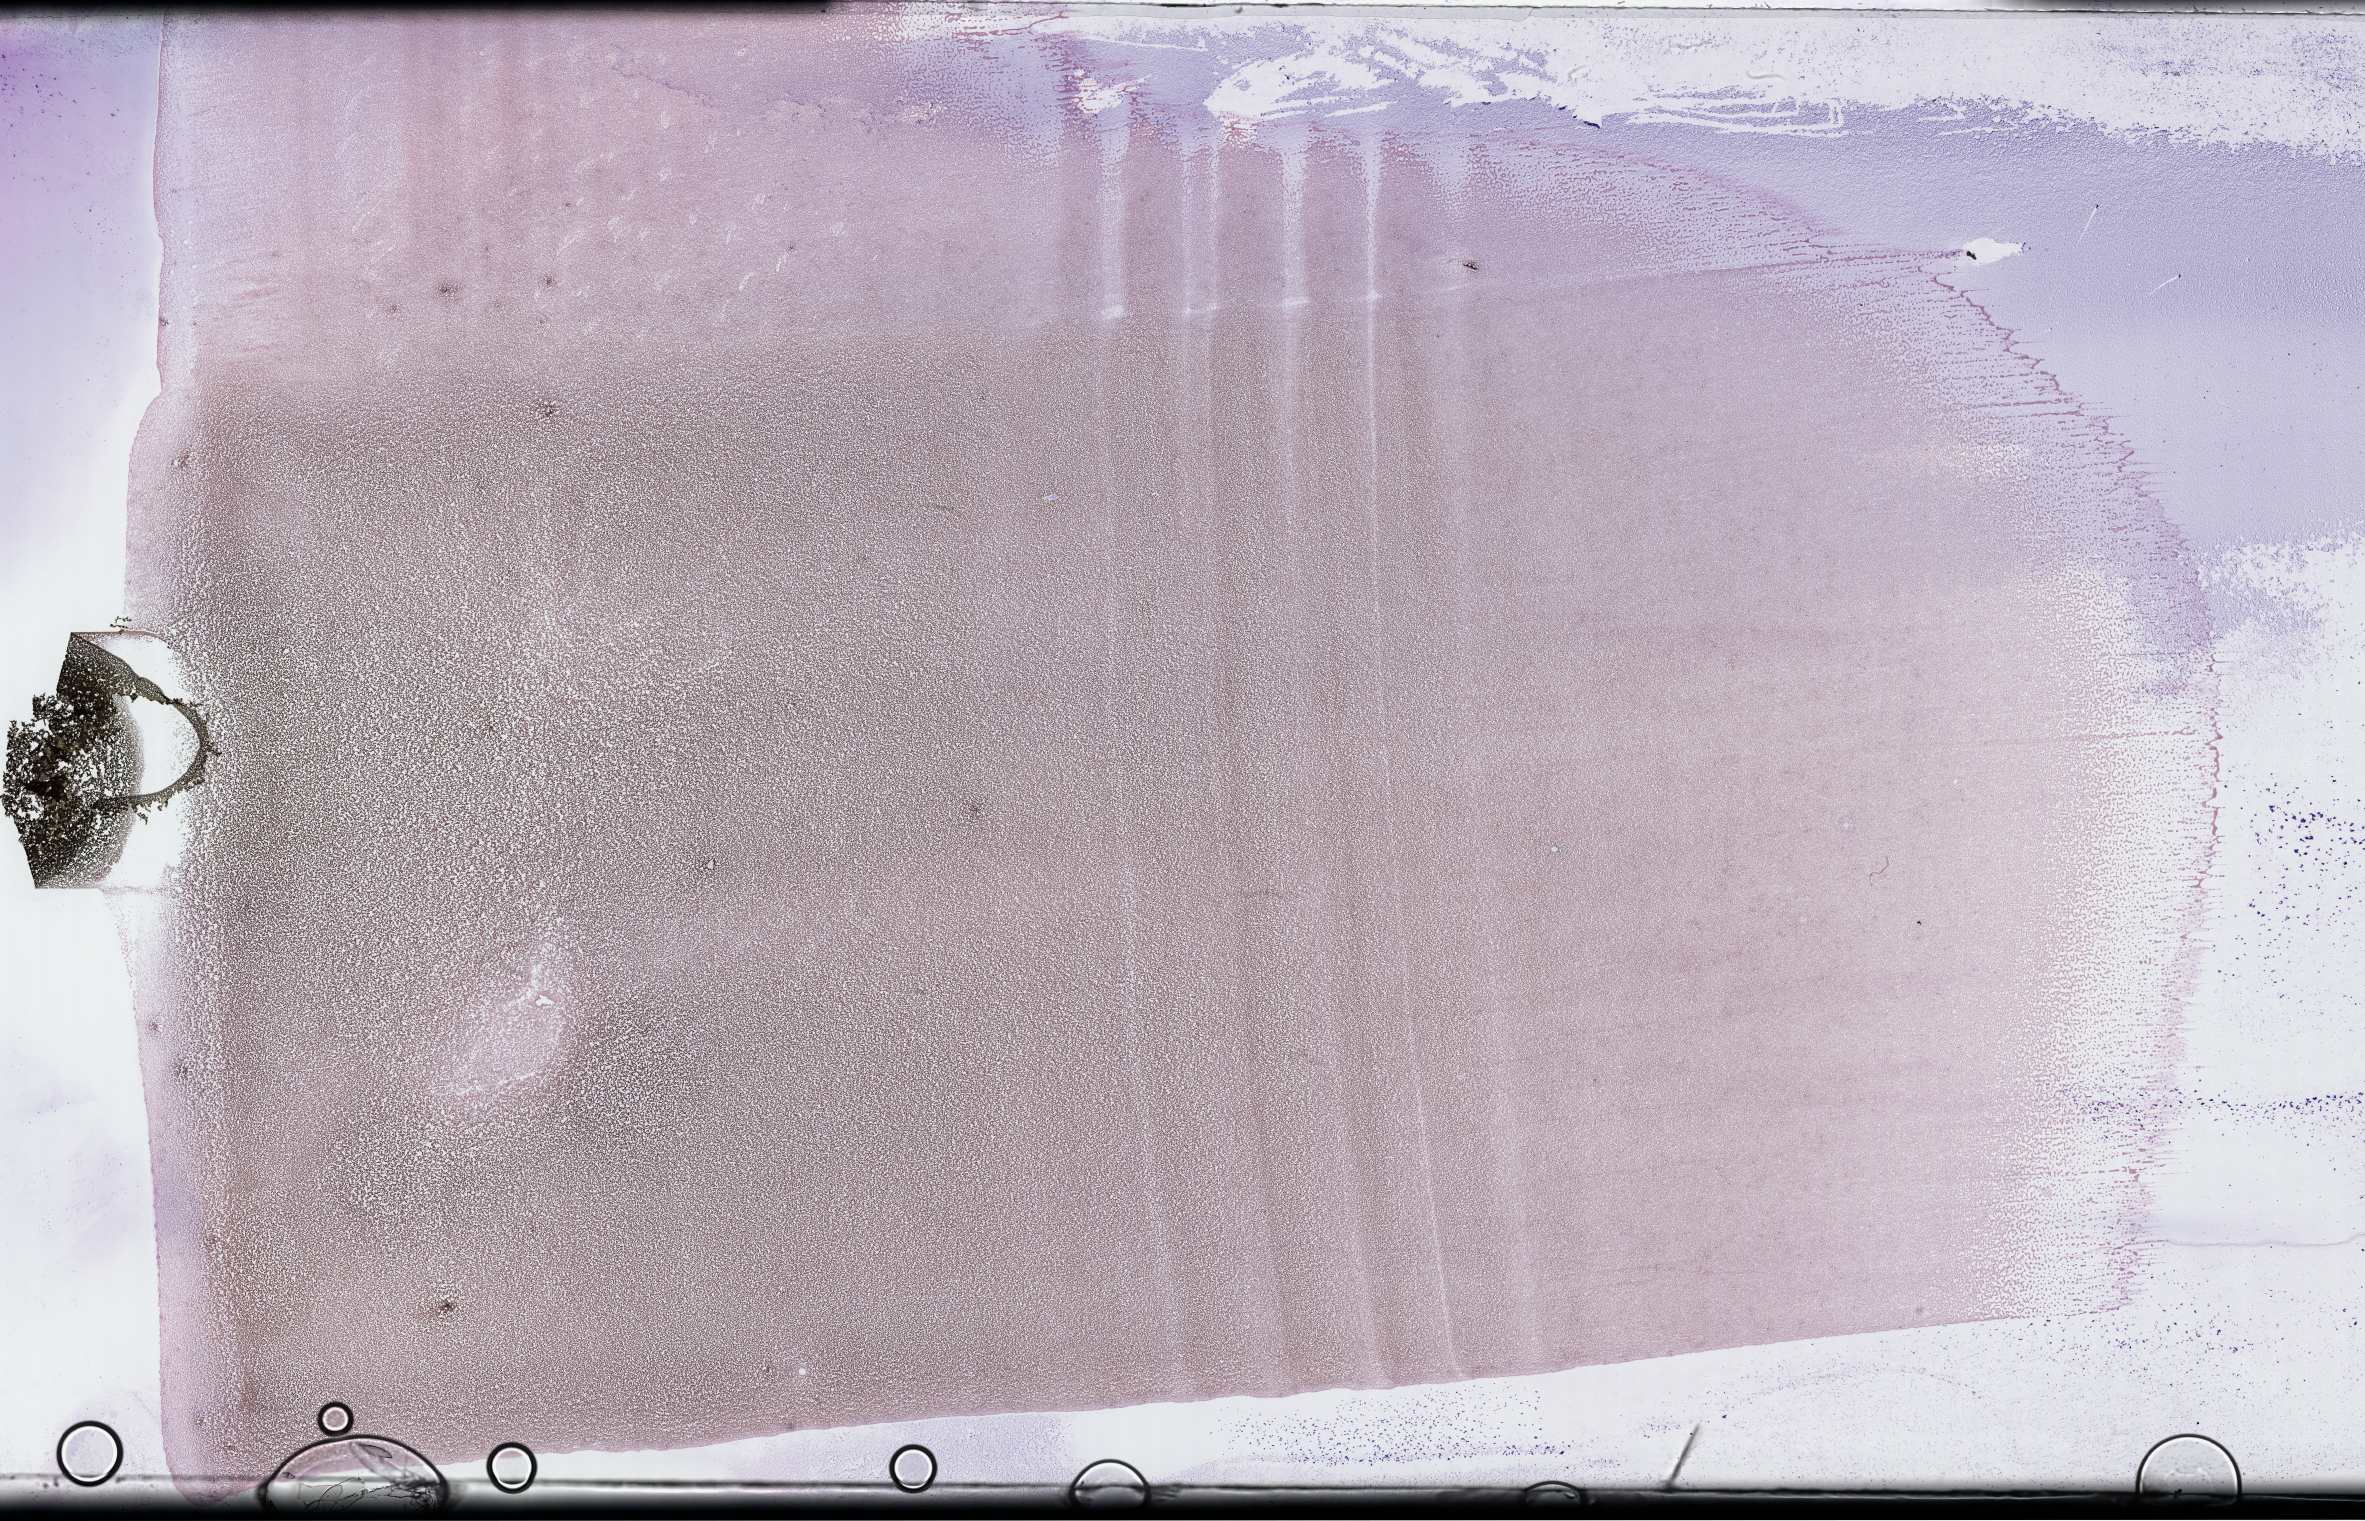
Whole-slide image of a whole blood smear, Wright-Giemsa stain — a low-resolution overview of the entire scanned area, about 38.2 x 24.6 mm; collected on treatment. Patient: male.
- from a patient with: Plasma Cell Myeloma